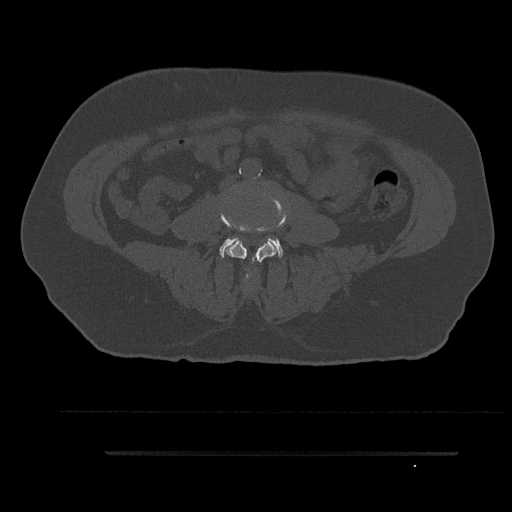
CT including the spine, one axial slice; position 12 of 797 along the scan axis; reconstruction kernel Br40s/3; 120 kVp; bone window (W 1800 / L 400 HU); 0.5 mm slice thickness; 512 × 512 image matrix. Male patient, age 63 years. From the clinical record (not read from this slice): primary cancer: renal.
Annotated regions visible in this slice (semi-automatically segmented with operator editing):
- L3 vertebra: box from (x=219, y=191) to (x=287, y=285) px
- L4 vertebra: (x=219, y=237)–(x=284, y=258)